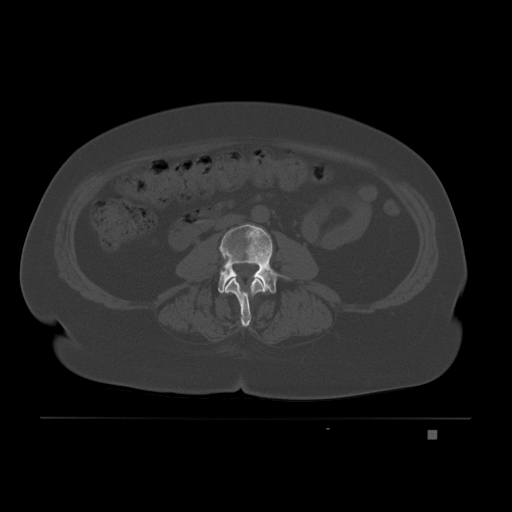
CT including the spine, one axial slice; bone window (W 1800 / L 400 HU); 3 mm slice thickness; 512 × 512 image matrix. Patient: female, 63 years. Case-level facts recorded for this patient, not image findings: primary cancer: breast.
Annotated regions visible in this slice (semi-automatic segmentation, software-assisted and operator-edited):
- L2 vertebra: bounding box <224,278,265,327> (left, top, right, bottom; pixels)
- L3 vertebra: <218,223,289,295>